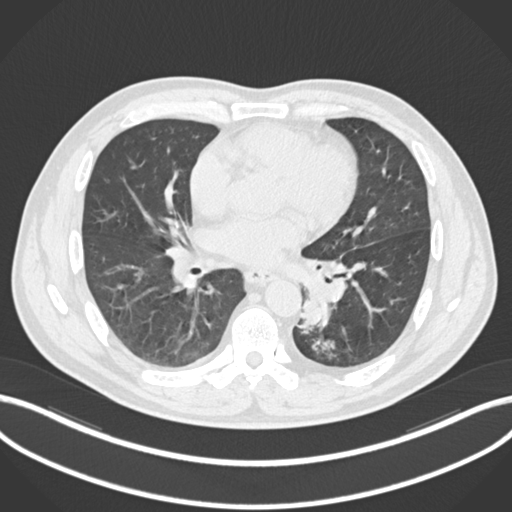
Chest CT, one axial slice; slice 105 of 223 in the series (ordered by position); reconstruction kernel B30f; lung window (W 1500 / L -600 HU); 512 × 512 image matrix, field of view 400 × 400 mm. Patient: male, 50 years. From the clinical record (not read from this slice): clinical TNM (as recorded): T2a N3 M0.
Structures marked on this image (bounding box drawn by a radiologist):
- lung tumour (recorded histology: squamous cell carcinoma): bounding box (x1, y1, x2, y2) in pixels: (299, 285, 331, 336)